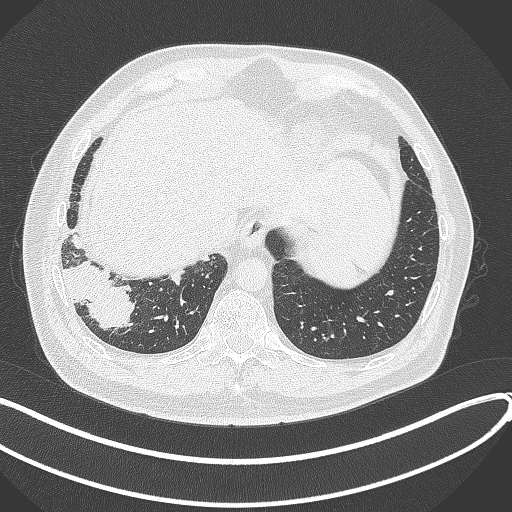
Chest CT, one axial slice. Slice 65 of 360 in the series (ordered by position). Reconstruction kernel B70f. Lung window (W 1500 / L -600 HU). 1 mm slice thickness. 512 × 512 image matrix, field of view 400 × 400 mm. Patient: male, 59 years.
Annotated regions visible in this slice (bounding box drawn by a radiologist):
- lung tumour (recorded histology: adenocarcinoma): bounding box <61,257,135,332> (left, top, right, bottom; pixels)